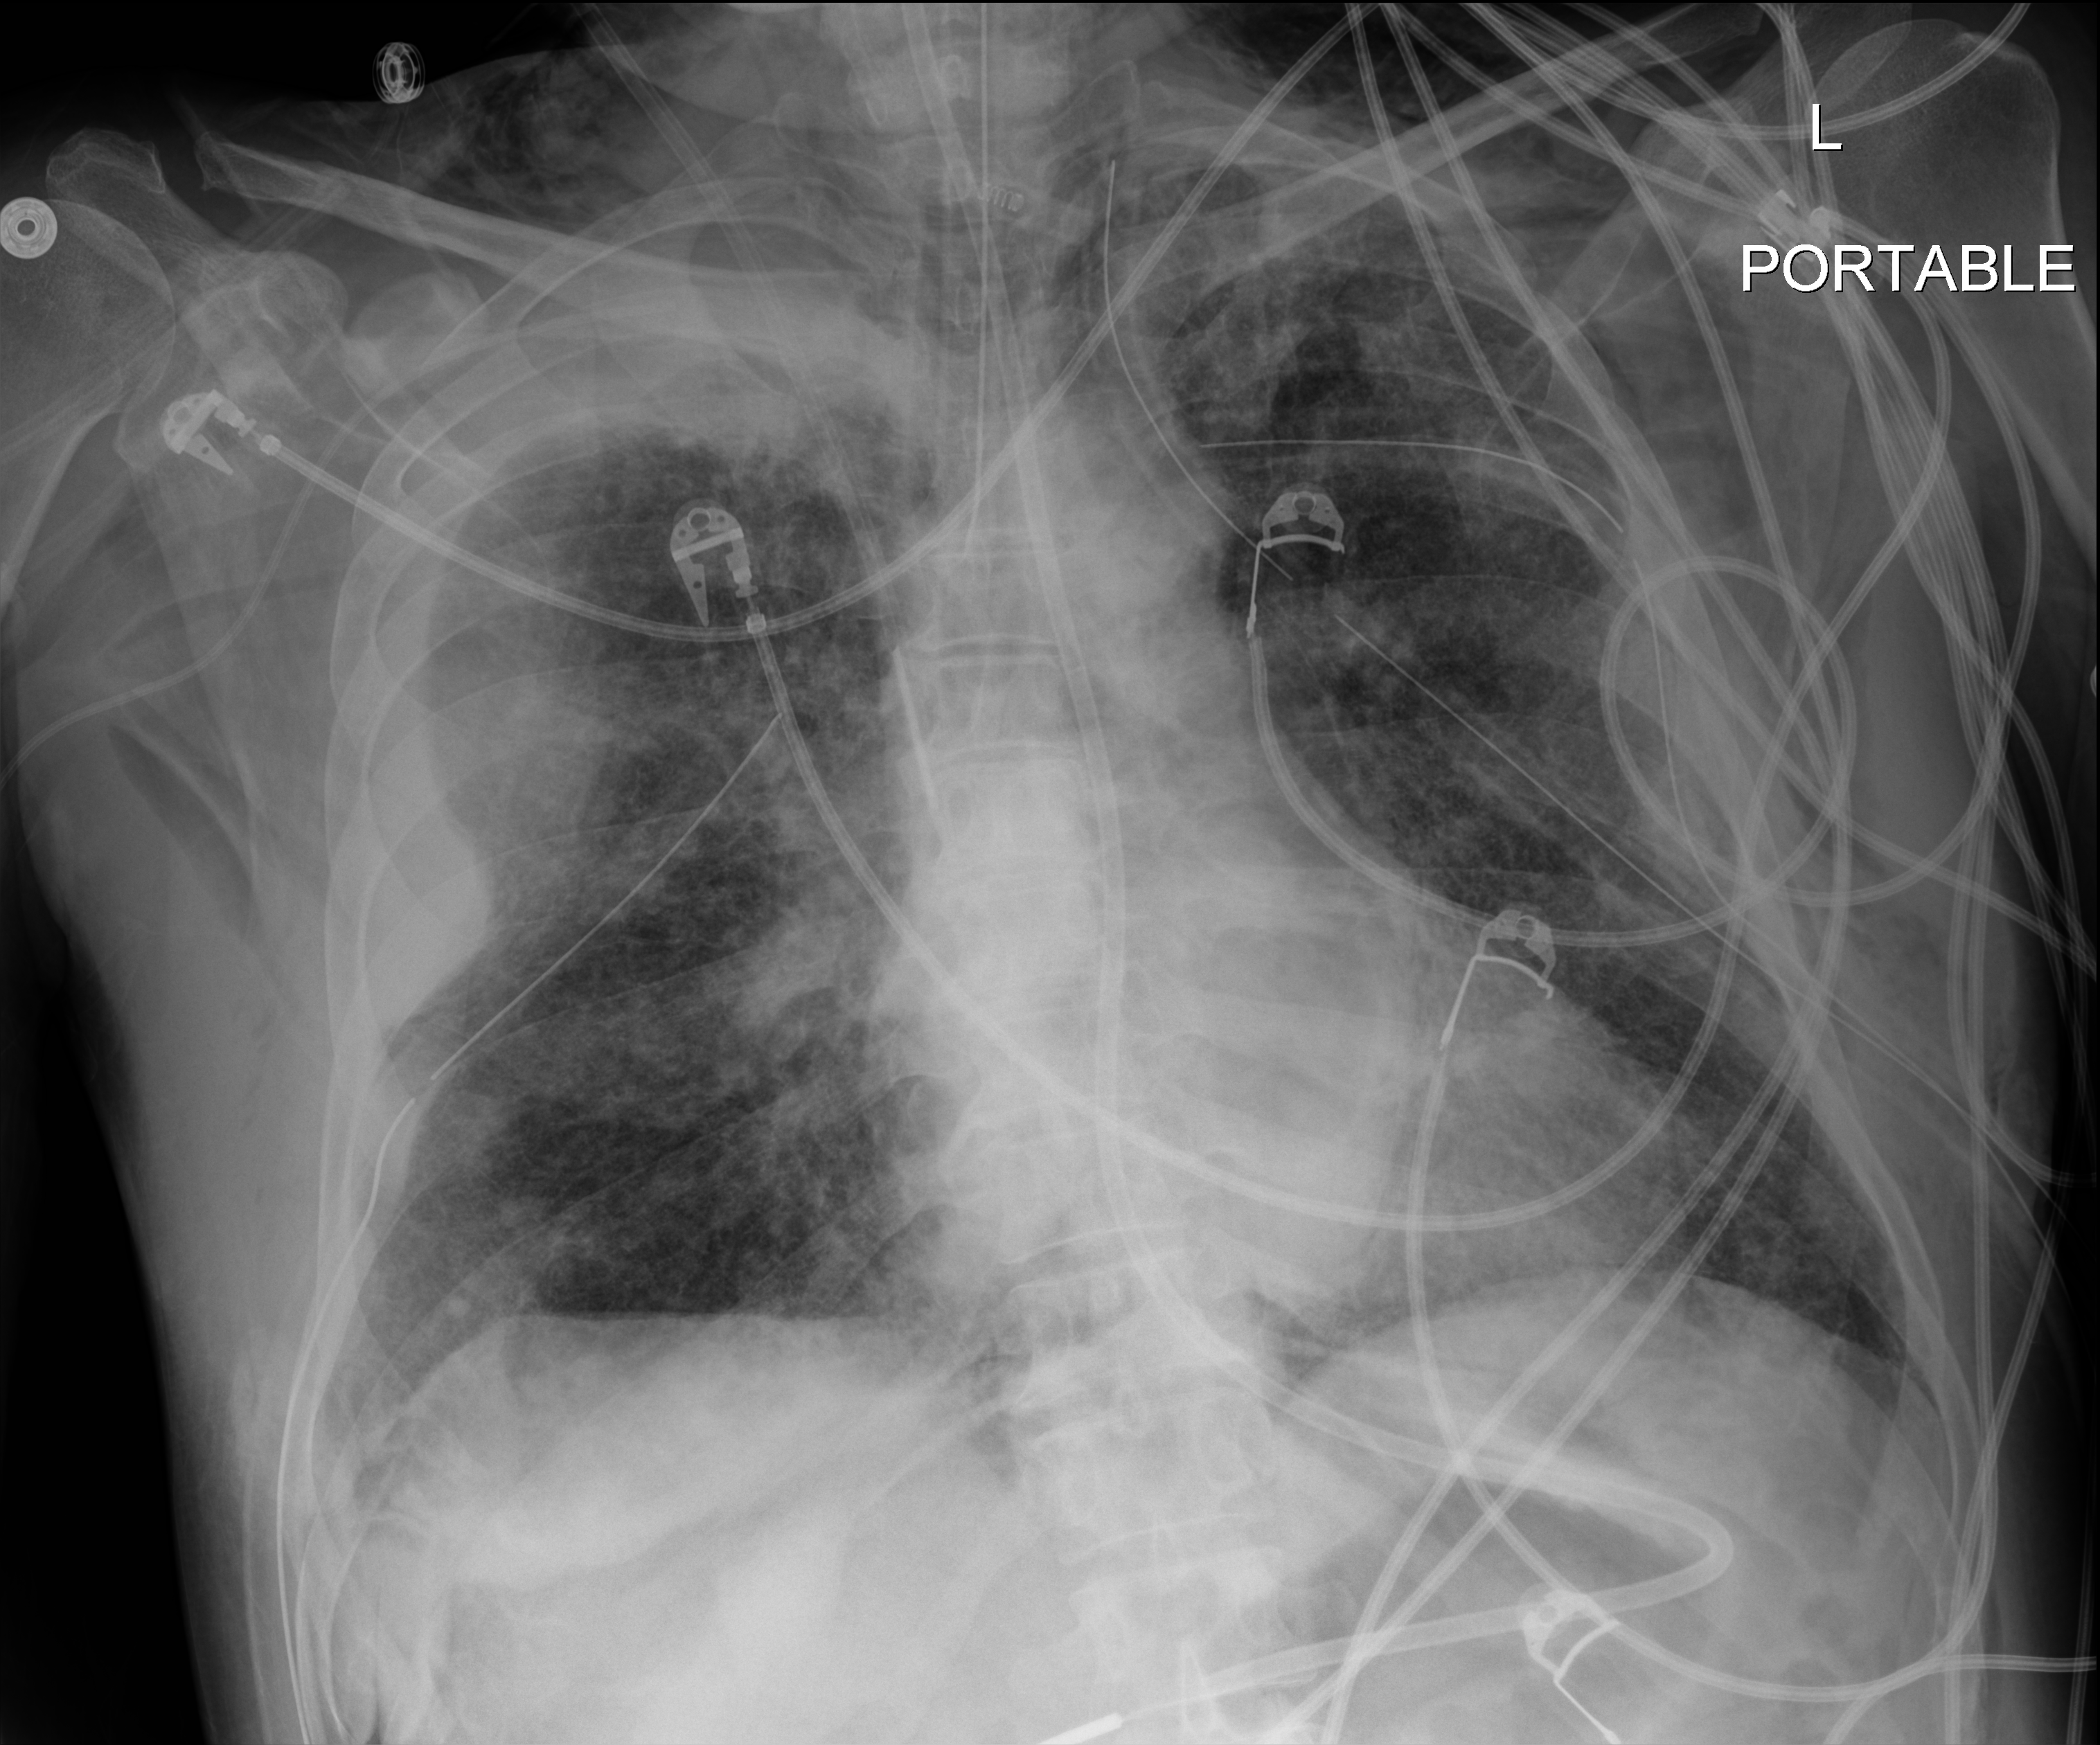
Bedside chest radiograph (digital radiography), anteroposterior (AP) projection. Male patient hospitalised with COVID-19, age 18–59 years.
Admission-level facts for this patient (not findings on this image; timing relative to this image not recorded):
- admitted to intensive care during this hospital stay: yes
- chronic kidney disease (admission record): no
- mechanically ventilated during this hospital stay: yes